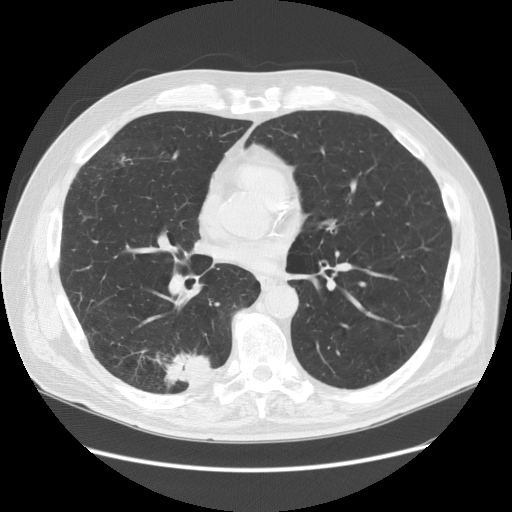
Low-dose screening chest CT, axial slice, baseline screening round, lung window (W 1500 / L -600 HU), 2.5 mm slice thickness, standard (soft-tissue) reconstruction kernel (STANDARD), slice 79 of 149 in the series. Male, age 68 years at enrolment. Former smoker at enrolment.
Expert-annotated lung lesion, bounding box (x1, y1, x2, y2) in pixels: (125, 337, 225, 410). The exam's reader record, not a measurement of the box and not confirmed to be the same lesion: non-calcified nodule or mass ≥4 mm, right lower lobe, 37 × 20 mm, spiculated (stellate) margins, soft tissue attenuation. Official screen result: positive, change unspecified: nodule(s) >= 4 mm or enlarging nodule(s), mass(es), or other non-specific abnormalities suspicious for lung cancer. Participant outcome: lung cancer diagnosed 24 days after this screen — adenosquamous carcinoma, right lower lobe, poorly differentiated (G3), stage IIIA (AJCC 6th edition), 30 mm at pathology.